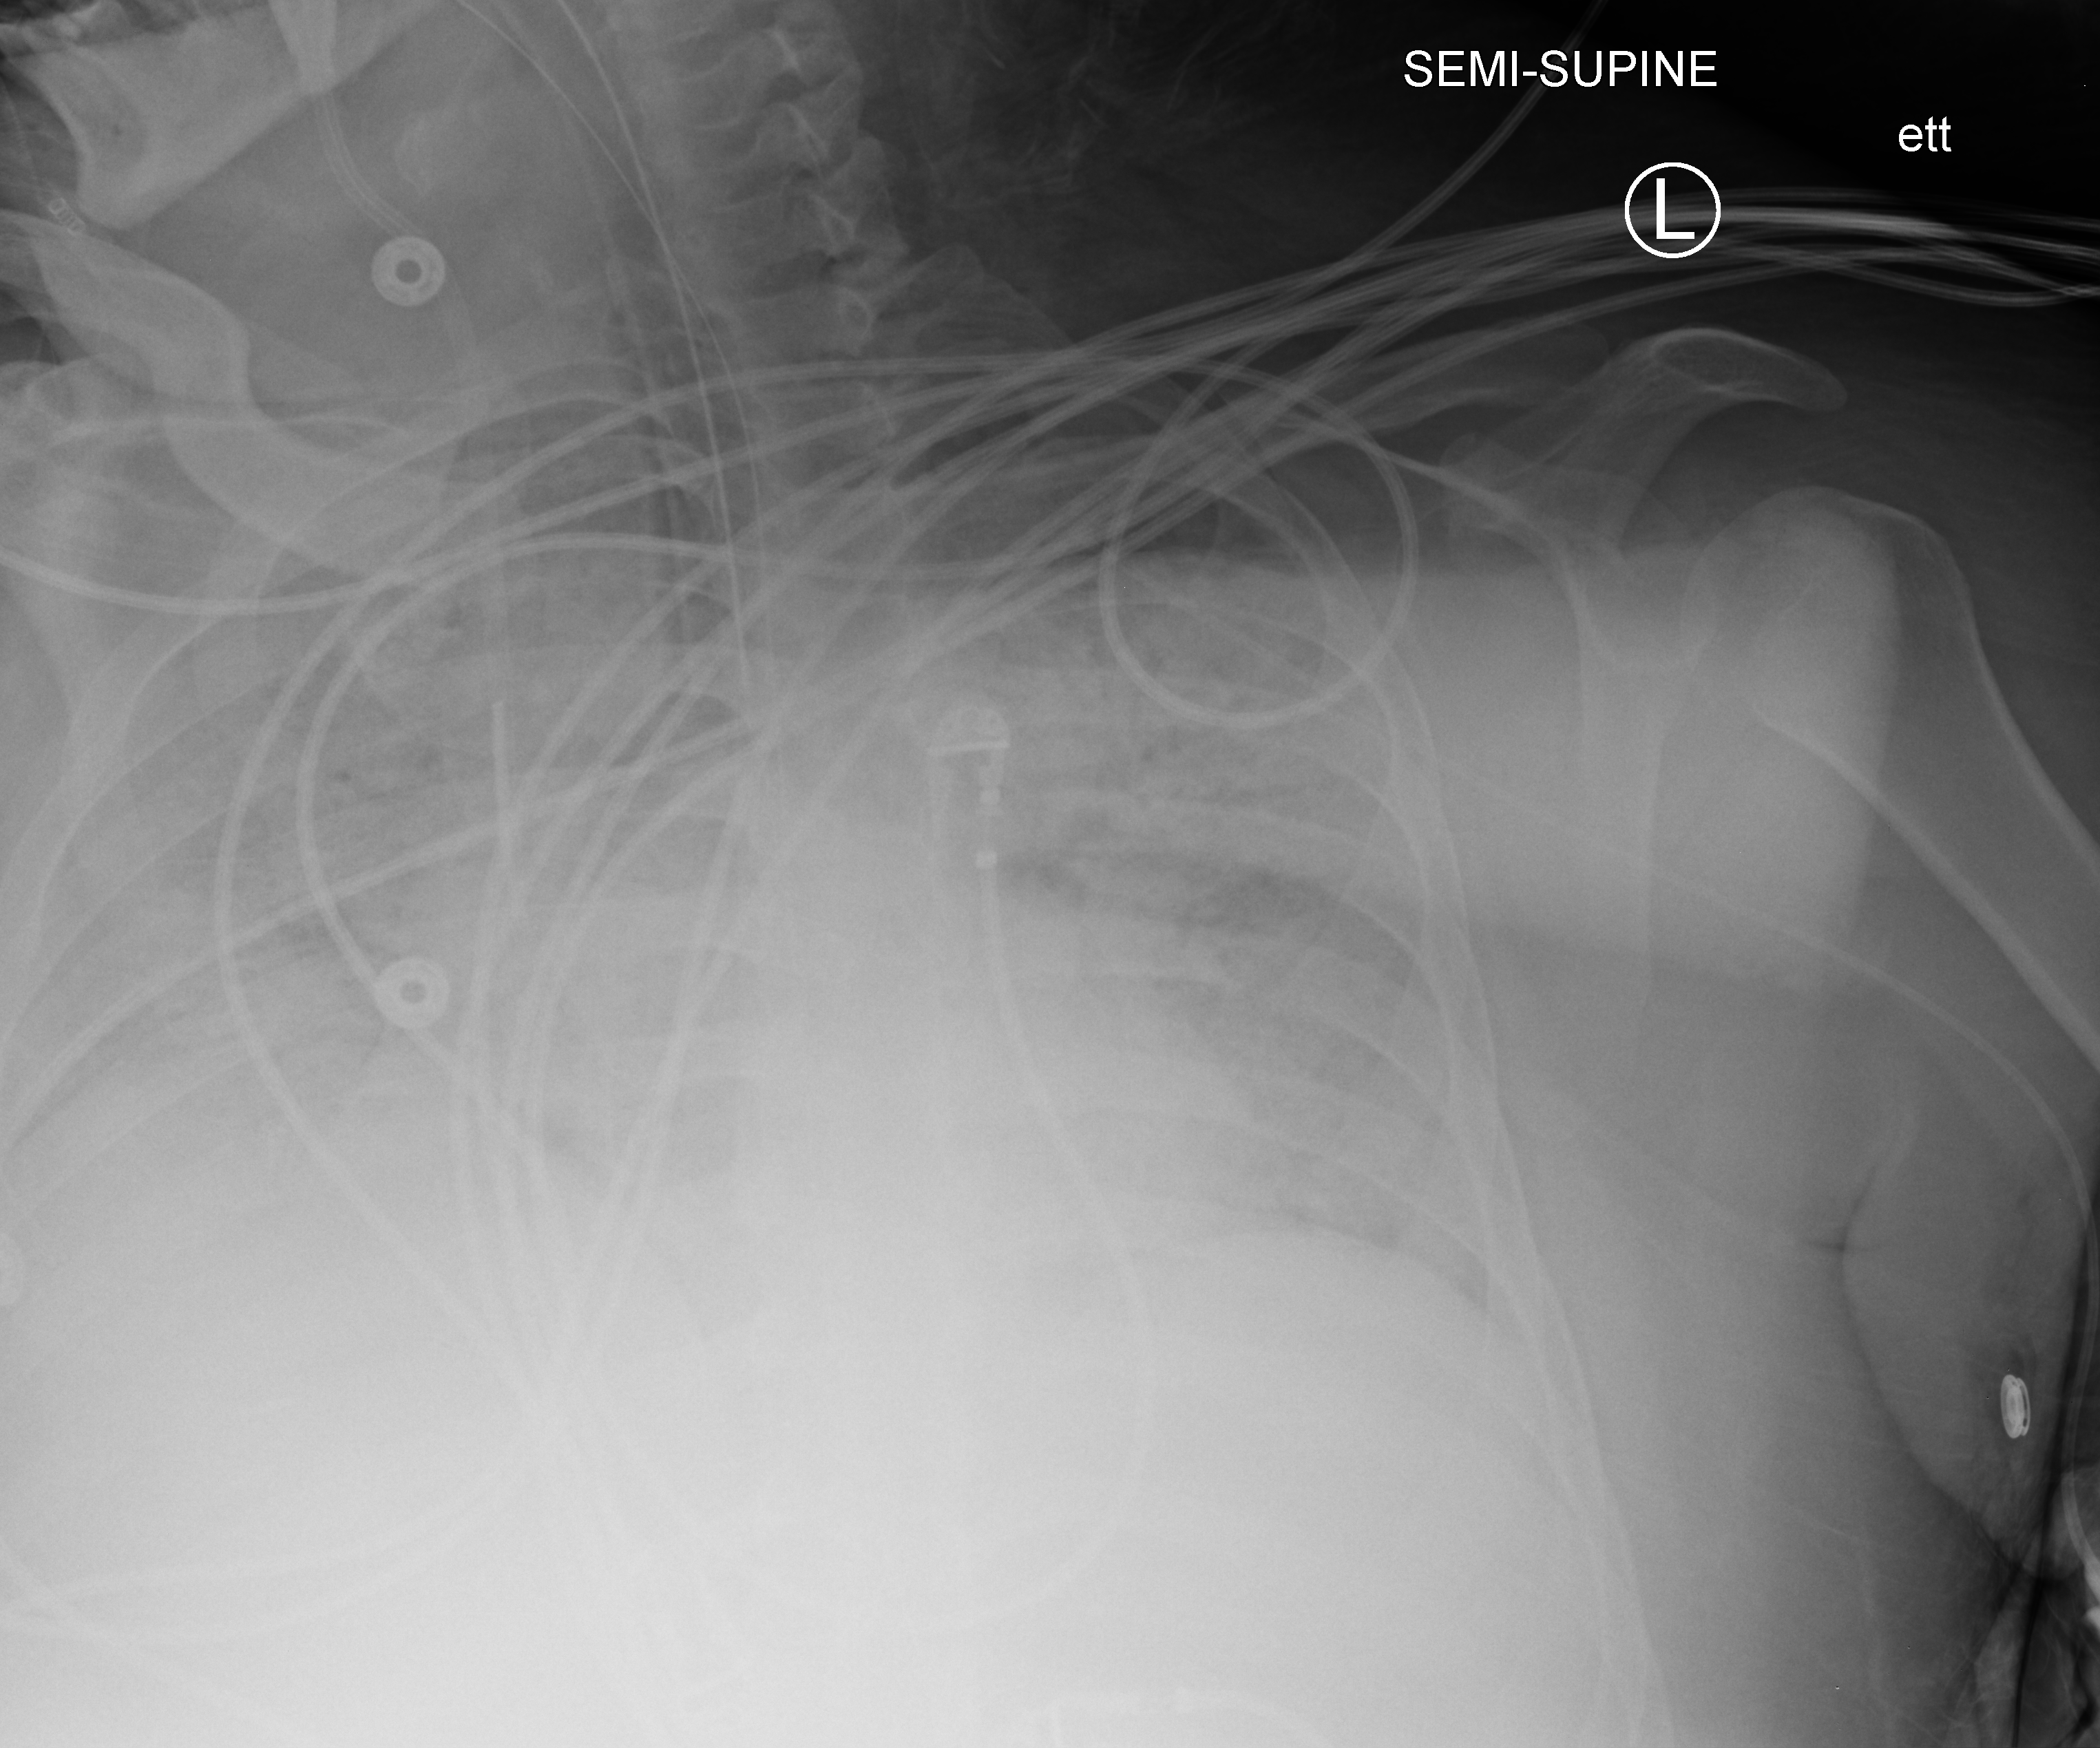
Chest X-ray (portable), anteroposterior (AP) projection. Adult patient hospitalised with COVID-19, age 18–59 years.
Admission-level facts for this patient (not findings on this image; timing relative to this image not recorded): admitted to intensive care during this hospital stay: yes.